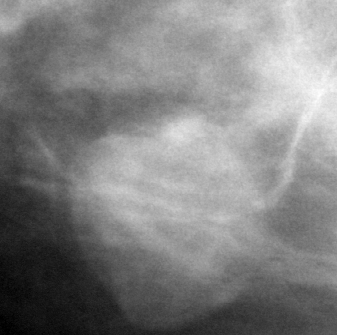
Cropped region of a digitized screen-film mammogram centred on a radiologist-marked abnormality, right breast, MLO view, BI-RADS breast density category 1 (scale 1–4).
Mass, shape oval, margins circumscribed; BI-RADS assessment category 4; pathology result (as recorded, not read from the image): benign.